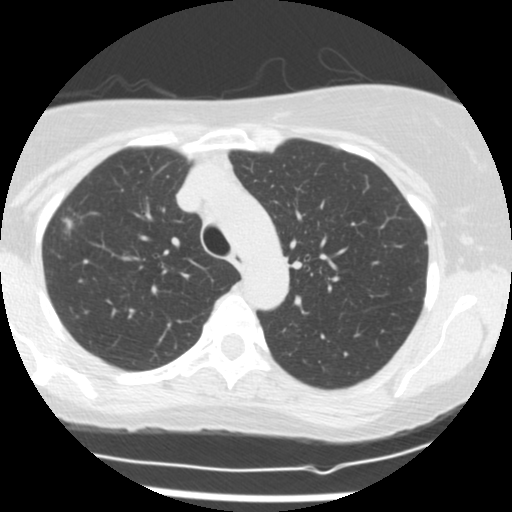
Low-dose screening chest CT, one axial slice. Lung window (W 1500 / L -600 HU). 2.5 mm slice thickness. 512 × 512 image matrix, field of view 300 × 300 mm.
Outlined on this slice (outlined manually by an expert reader):
- lesion 1 (tumor, upper lobe of right lung): box from (x=63, y=218) to (x=73, y=229) px